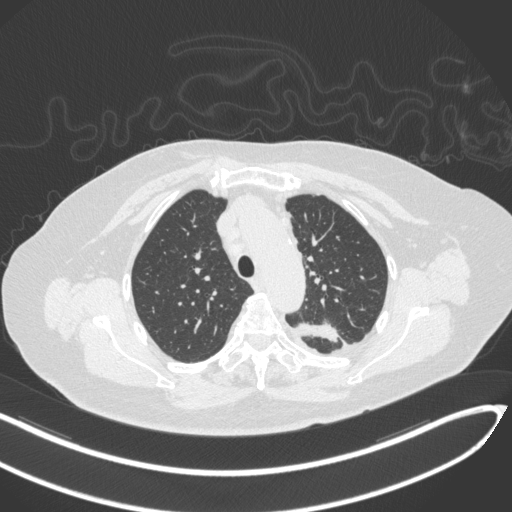
Chest CT, one axial slice; slice 238 of 270 in the series (ordered by position); reconstruction kernel B31f; 120 kVp; lung window (W 1500 / L -600 HU); 1 mm slice thickness; 512 × 512 image matrix, field of view 400 × 400 mm. Female patient, age 76 years. Case-level facts recorded for this patient, not image findings: clinical TNM (as recorded): T1c N0 M0.
Structures marked on this image (bounding box drawn by a radiologist):
- lung tumour (recorded histology: adenocarcinoma): bounding box <292,319,340,345> (left, top, right, bottom; pixels)